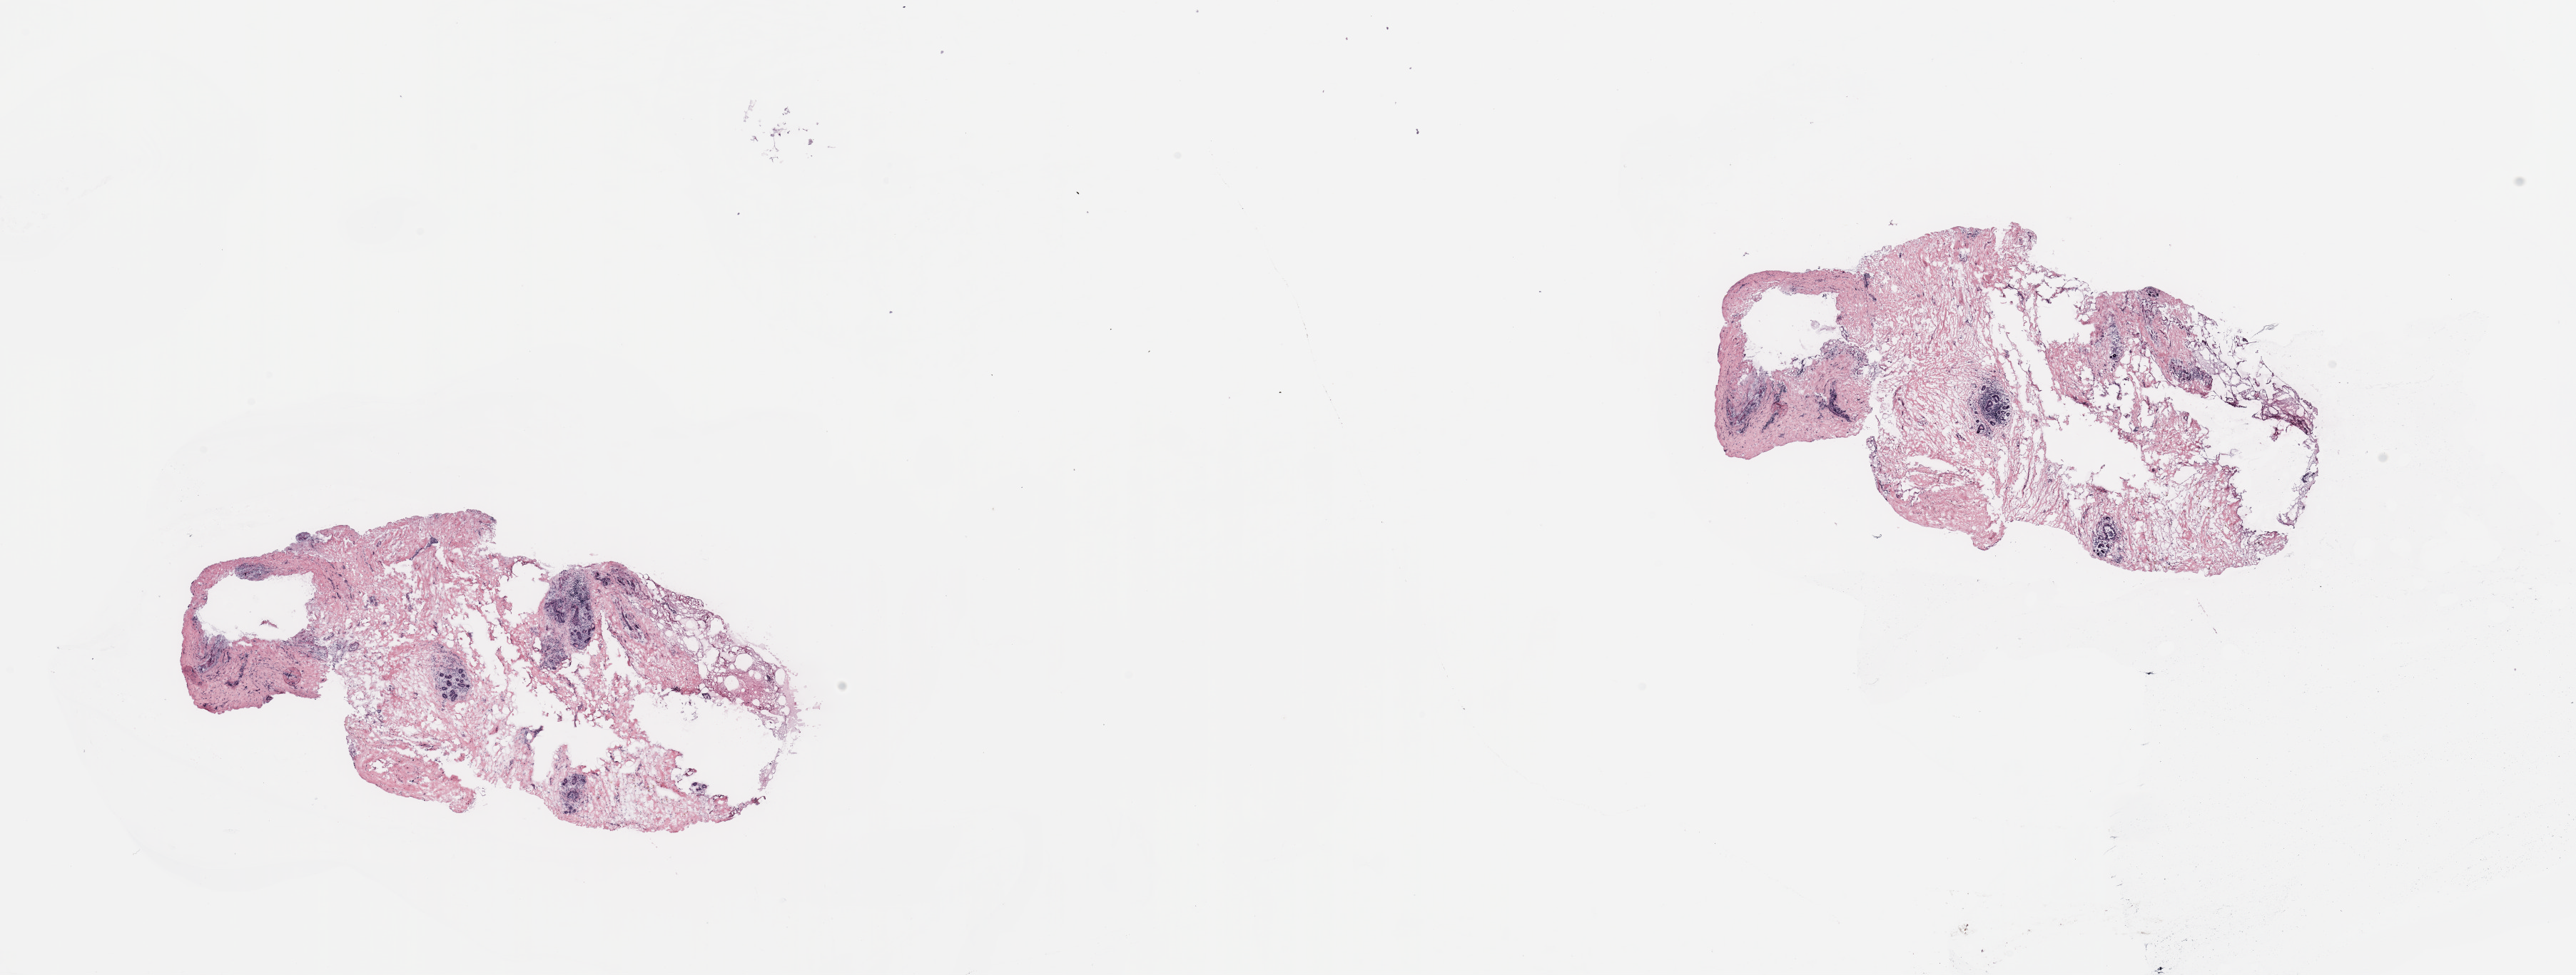
Whole-slide histology image, H&E — low-resolution overview of the scanned area, about 28.5 x 10.8 mm (from a 20x scan), breast, tumour tissue. 55-year-old female patient.
Diagnosis: Infiltrating duct carcinoma, NOS. AJCC pathologic stage: IIB.